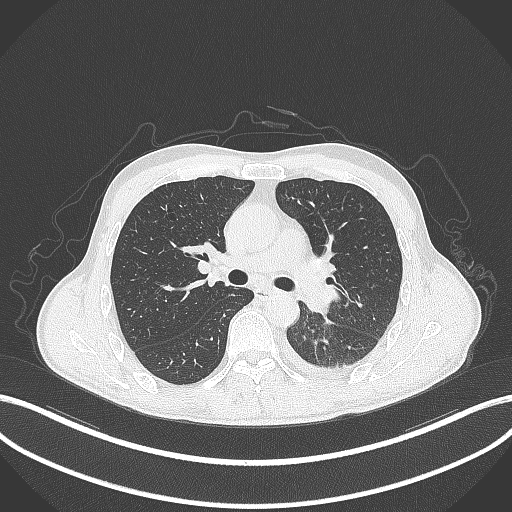
Chest CT, one axial slice. Position 201 of 295 along the scan axis. Reconstruction kernel B70f. 120 kVp. Lung window (W 1500 / L -600 HU). 512 × 512 image matrix. Patient: male, 47 years. Case-level facts recorded for this patient, not image findings: clinical TNM (as recorded): T3 N1 M1c.
Outlined on this slice (rectangle marked by the reading radiologist):
- lung tumour (recorded histology: small cell carcinoma): bounding box <296,276,342,316> (left, top, right, bottom; pixels)